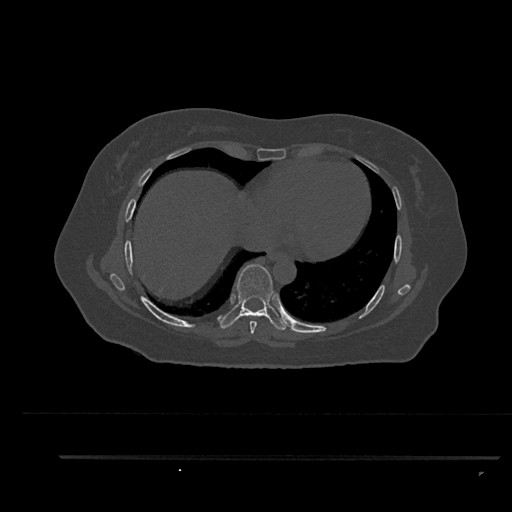
CT including the spine, one axial slice. Position 473 of 797 along the scan axis. Reconstruction kernel Br40s/3. 120 kVp. Bone window (W 1800 / L 400 HU). 0.5 mm slice thickness. 512 × 512 image matrix, field of view 408 × 408 mm. Patient: female, 44 years. From the clinical record (not read from this slice): primary cancer: renal; vertebrae with lytic lesions (as recorded): L1.
Structures marked on this image (semi-automatic segmentation, software-assisted and operator-edited):
- T7 vertebra: bounding box <249,321,257,334> (left, top, right, bottom; pixels)
- T8 vertebra: <218,264,287,330>